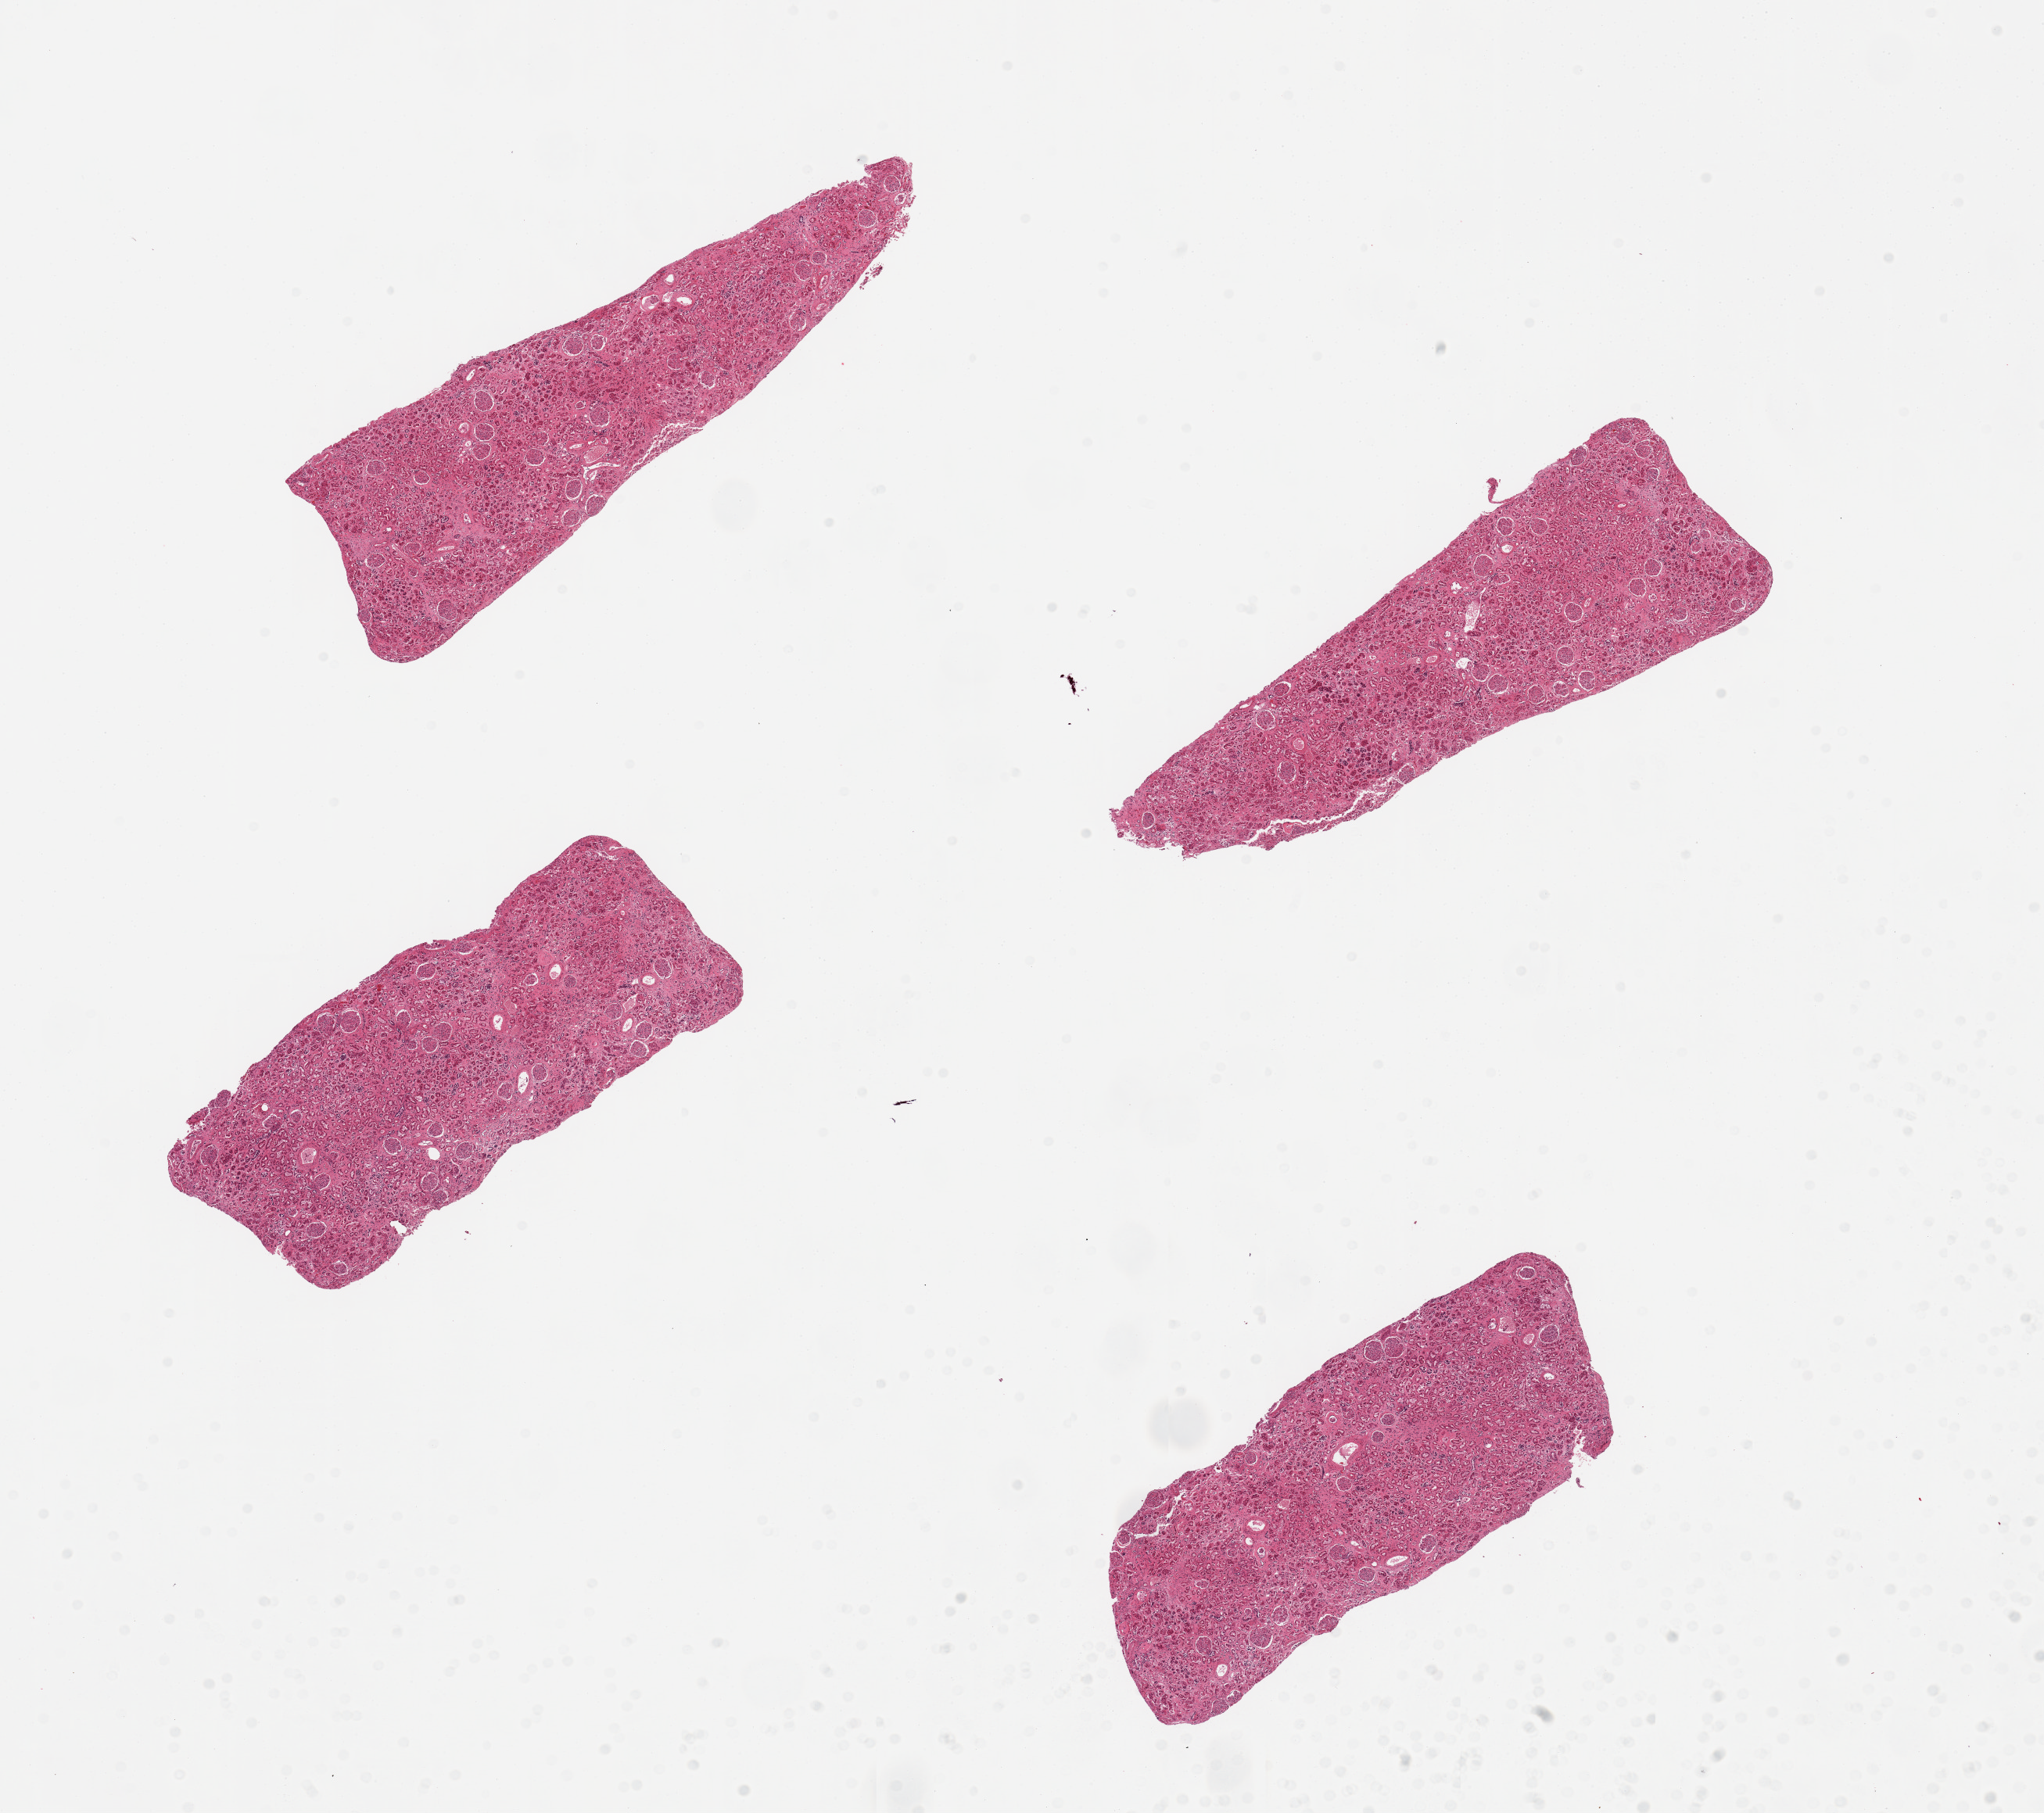
Digitized haematoxylin and eosin-stained section — whole scanned area (about 20.7 x 18.3 mm, acquisition: 20x scan) shown as a low-resolution overview, PAXgene-fixed paraffin-embedded (PFPE) section, target tissue: renal cortex, tissue donor sample. Male donor.
Reviewer comment on this tissue sample: 4 pieces; glomeruli in all sections, some interstitial fibrosis and vascular thickening, rare sclerotic glomerulus.